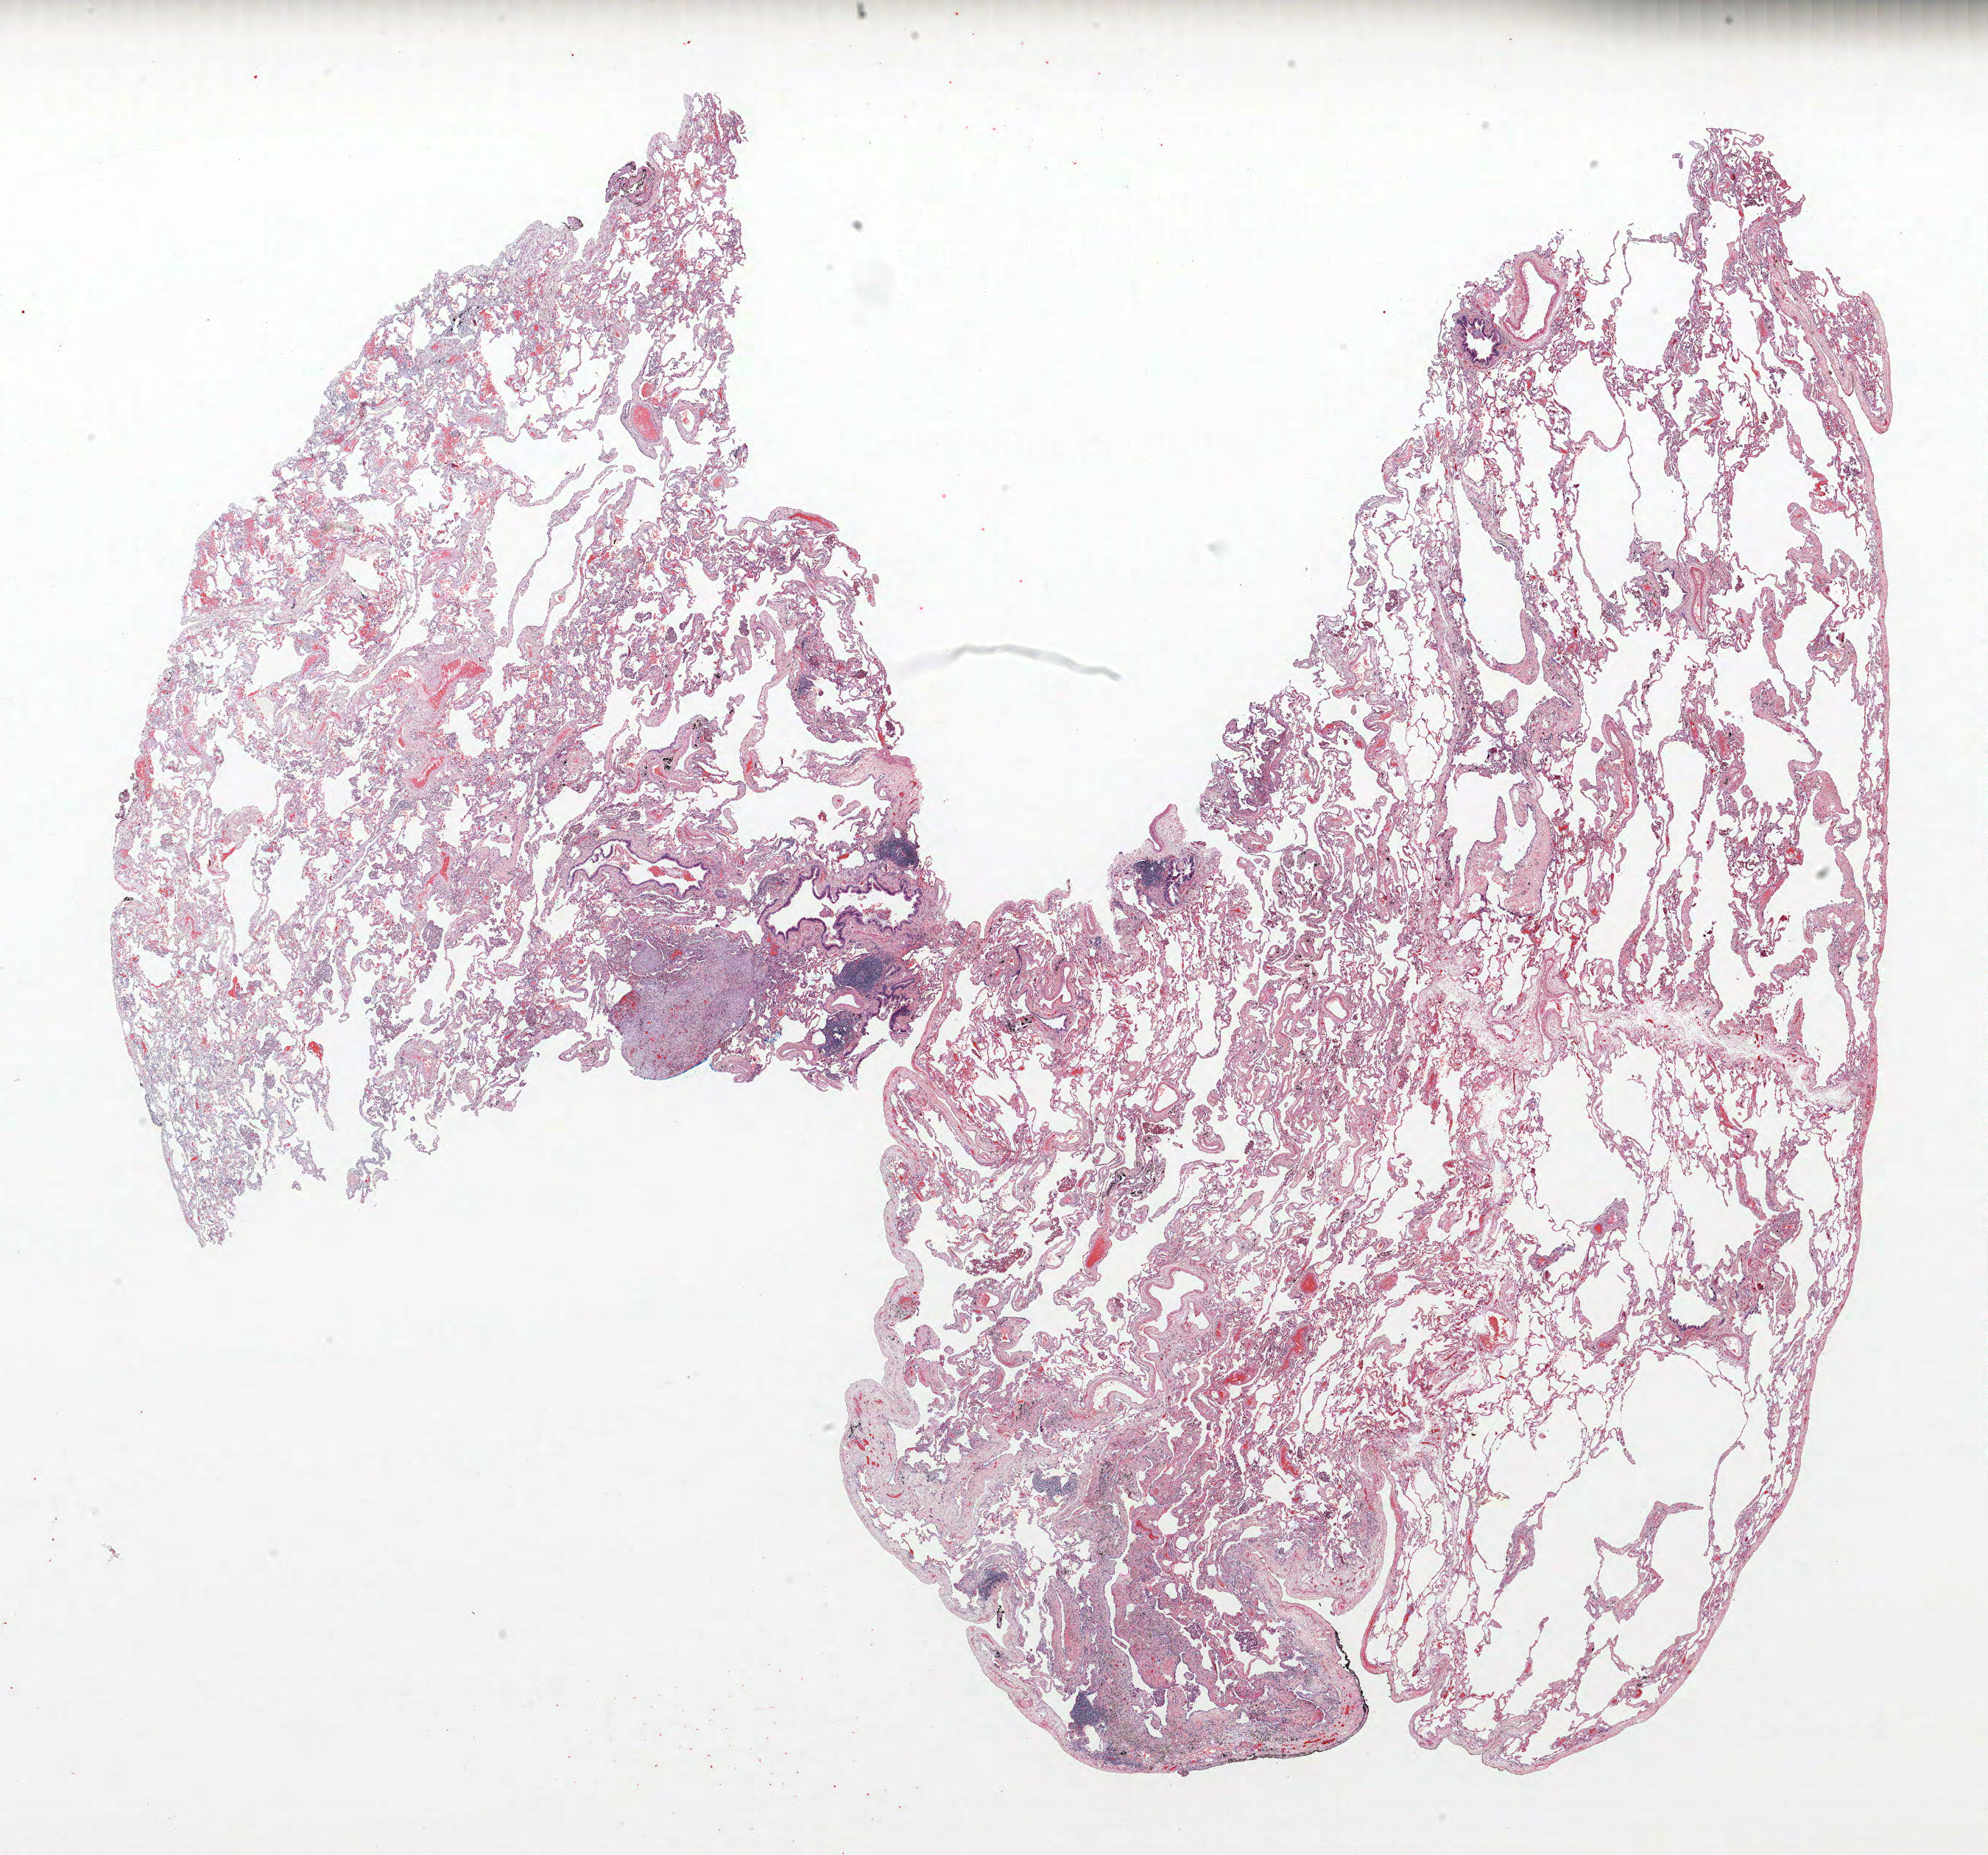
Hematoxylin and eosin (H&E) stained whole-slide image, shown as a low-resolution overview of the whole scanned area (about 21.6 x 20.2 mm, from a 40x scan). Formalin-fixed paraffin-embedded (FFPE) section. Lung. Female, age 64 at enrolment. Current smoker at enrolment. Grade: poorly differentiated (G3).
ICD-O-3 topography: upper lobe of lung (C34.1). Participant's lung-cancer diagnosis: Adenocarcinoma, NOS. Stage (AJCC 6th edition): IA. Primary tumour location (clinical record): left upper lobe. Tumour size (pathology): 12 mm.